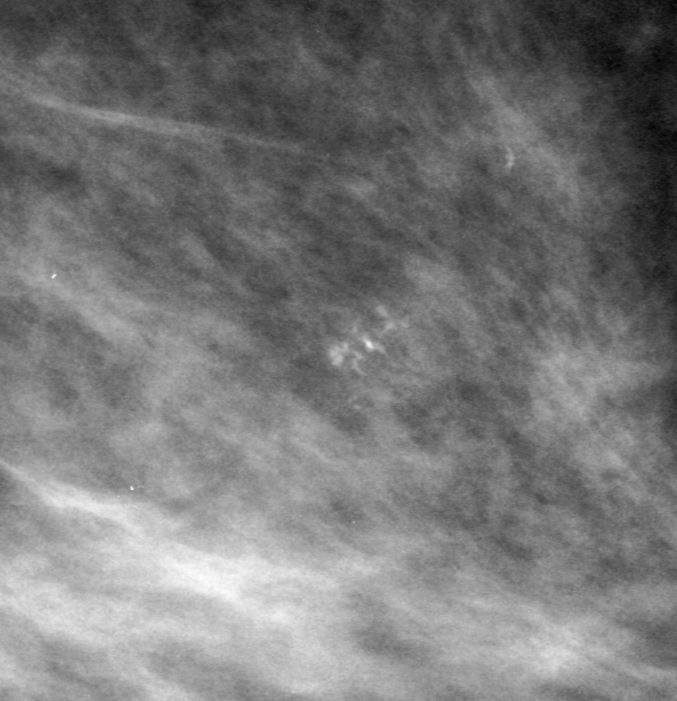
Cropped region of a digitized screen-film mammogram centred on a radiologist-marked abnormality; left breast; MLO view; BI-RADS breast density category 2 (scale 1–4).
Marked abnormality: calcifications, morphology pleomorphic, distribution clustered; BI-RADS assessment category 3; subtlety rating 3 on a 1 (subtle) to 5 (obvious) scale; pathology (as recorded): malignant.